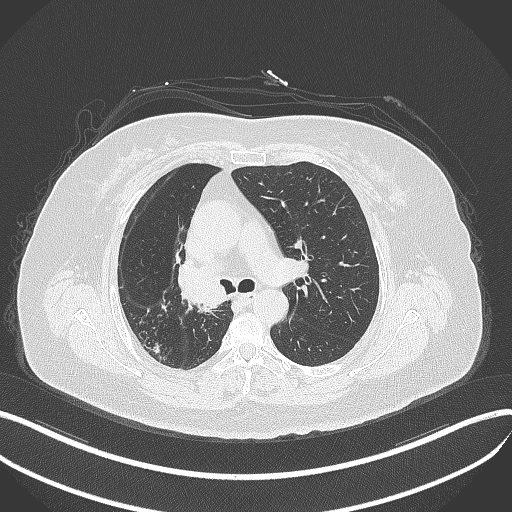
Chest CT, one axial slice; position 231 of 376 along the scan axis; 120 kVp; lung window (W 1500 / L -600 HU); 1 mm slice thickness; 512 × 512 image matrix, field of view 400 × 400 mm. Female patient, age 60 years. Case-level facts recorded for this patient, not image findings: clinical TNM (as recorded): T1c N0 M0; histopathological grade: G1-G2.
Annotated regions visible in this slice (bounding box drawn by a radiologist):
- lung tumour (recorded histology: squamous cell carcinoma): box from (x=174, y=260) to (x=235, y=311) px